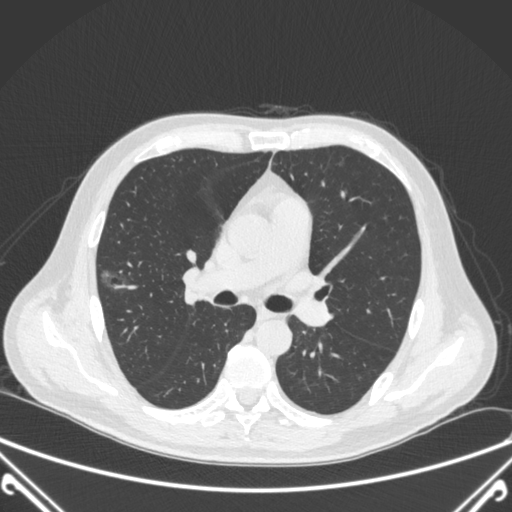
Chest CT, one axial slice; slice 221 of 360 in the series (ordered by position); lung window (W 1500 / L -600 HU); 1 mm slice thickness; 512 × 512 image matrix. Male patient, age 64 years. From the clinical record (not read from this slice): clinical TNM (as recorded): T1c N0 M0.
Annotated regions visible in this slice (bounding box drawn by a radiologist):
- lung tumour (recorded histology: adenocarcinoma): bounding box <100,263,134,296> (left, top, right, bottom; pixels)